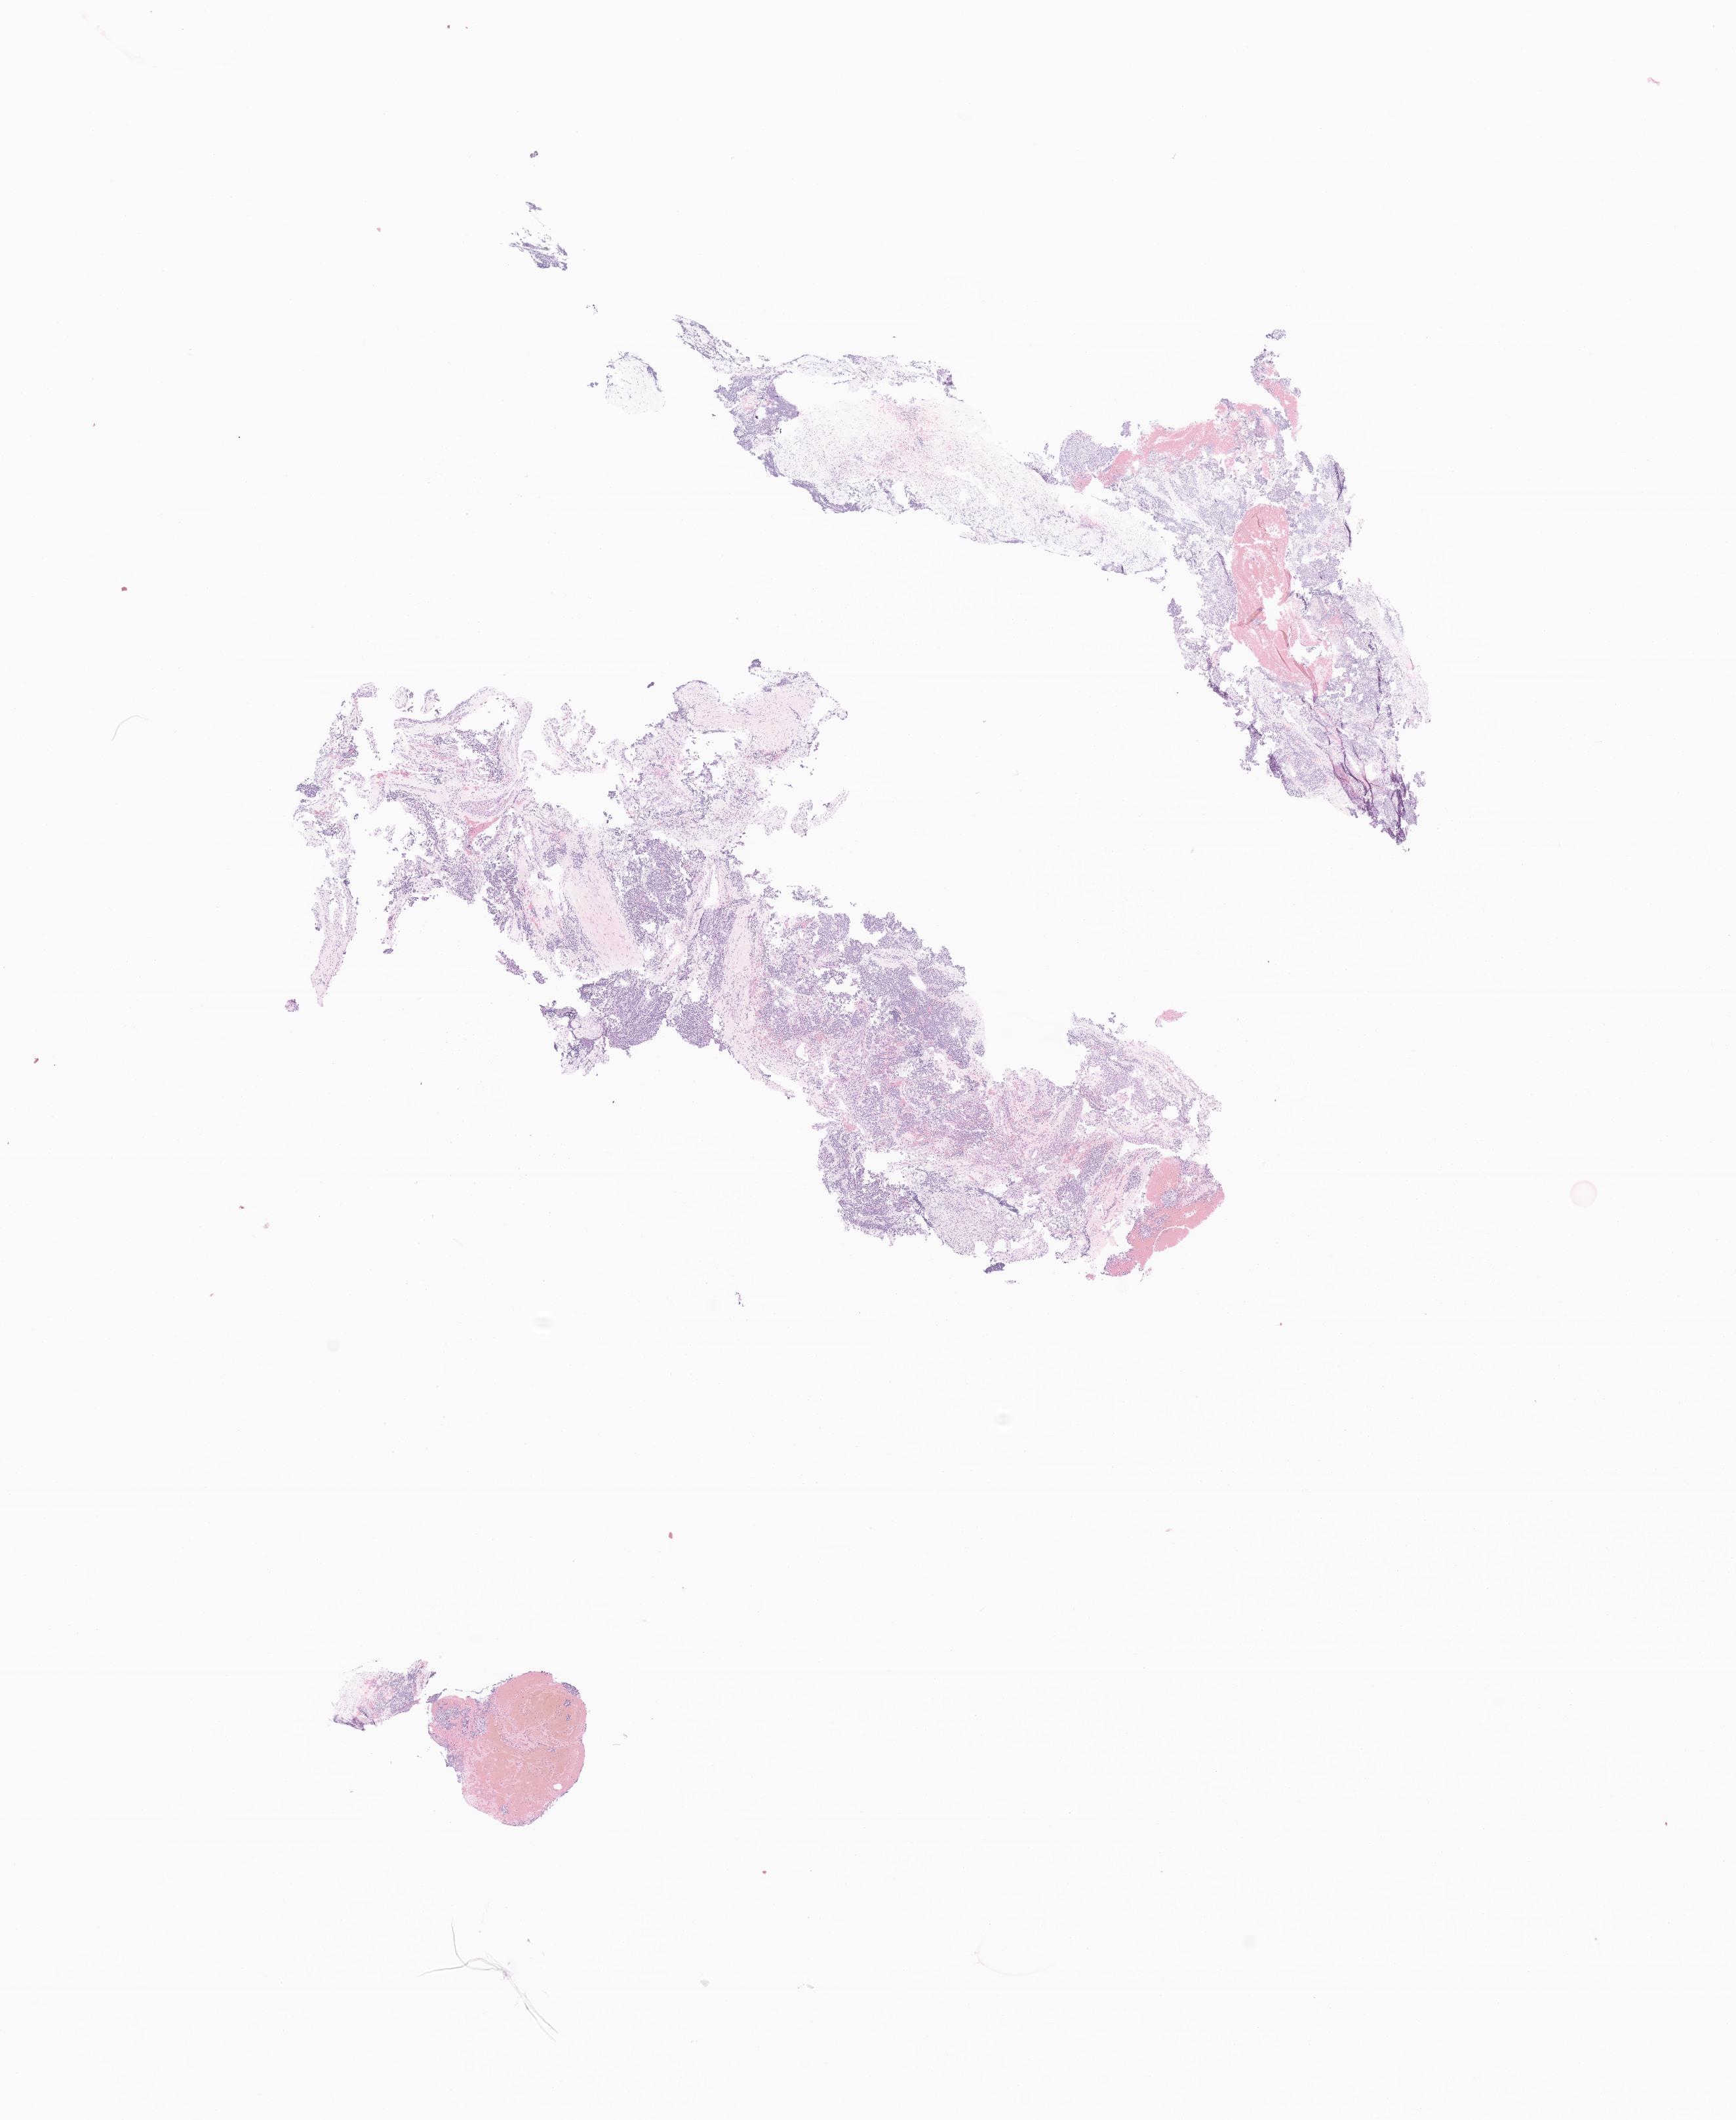
Haematoxylin and eosin whole-slide image of tumor tissue from the adrenal gland — shown as a low-resolution overview of the whole scanned area (about 11.2 x 13.6 mm). Formalin-fixed, paraffin-embedded (FFPE) tissue. Patient: female, age 665 days (about 1.8 years).
* diagnosis (ICD-O-3 morphology term): Neuroblastoma, NOS